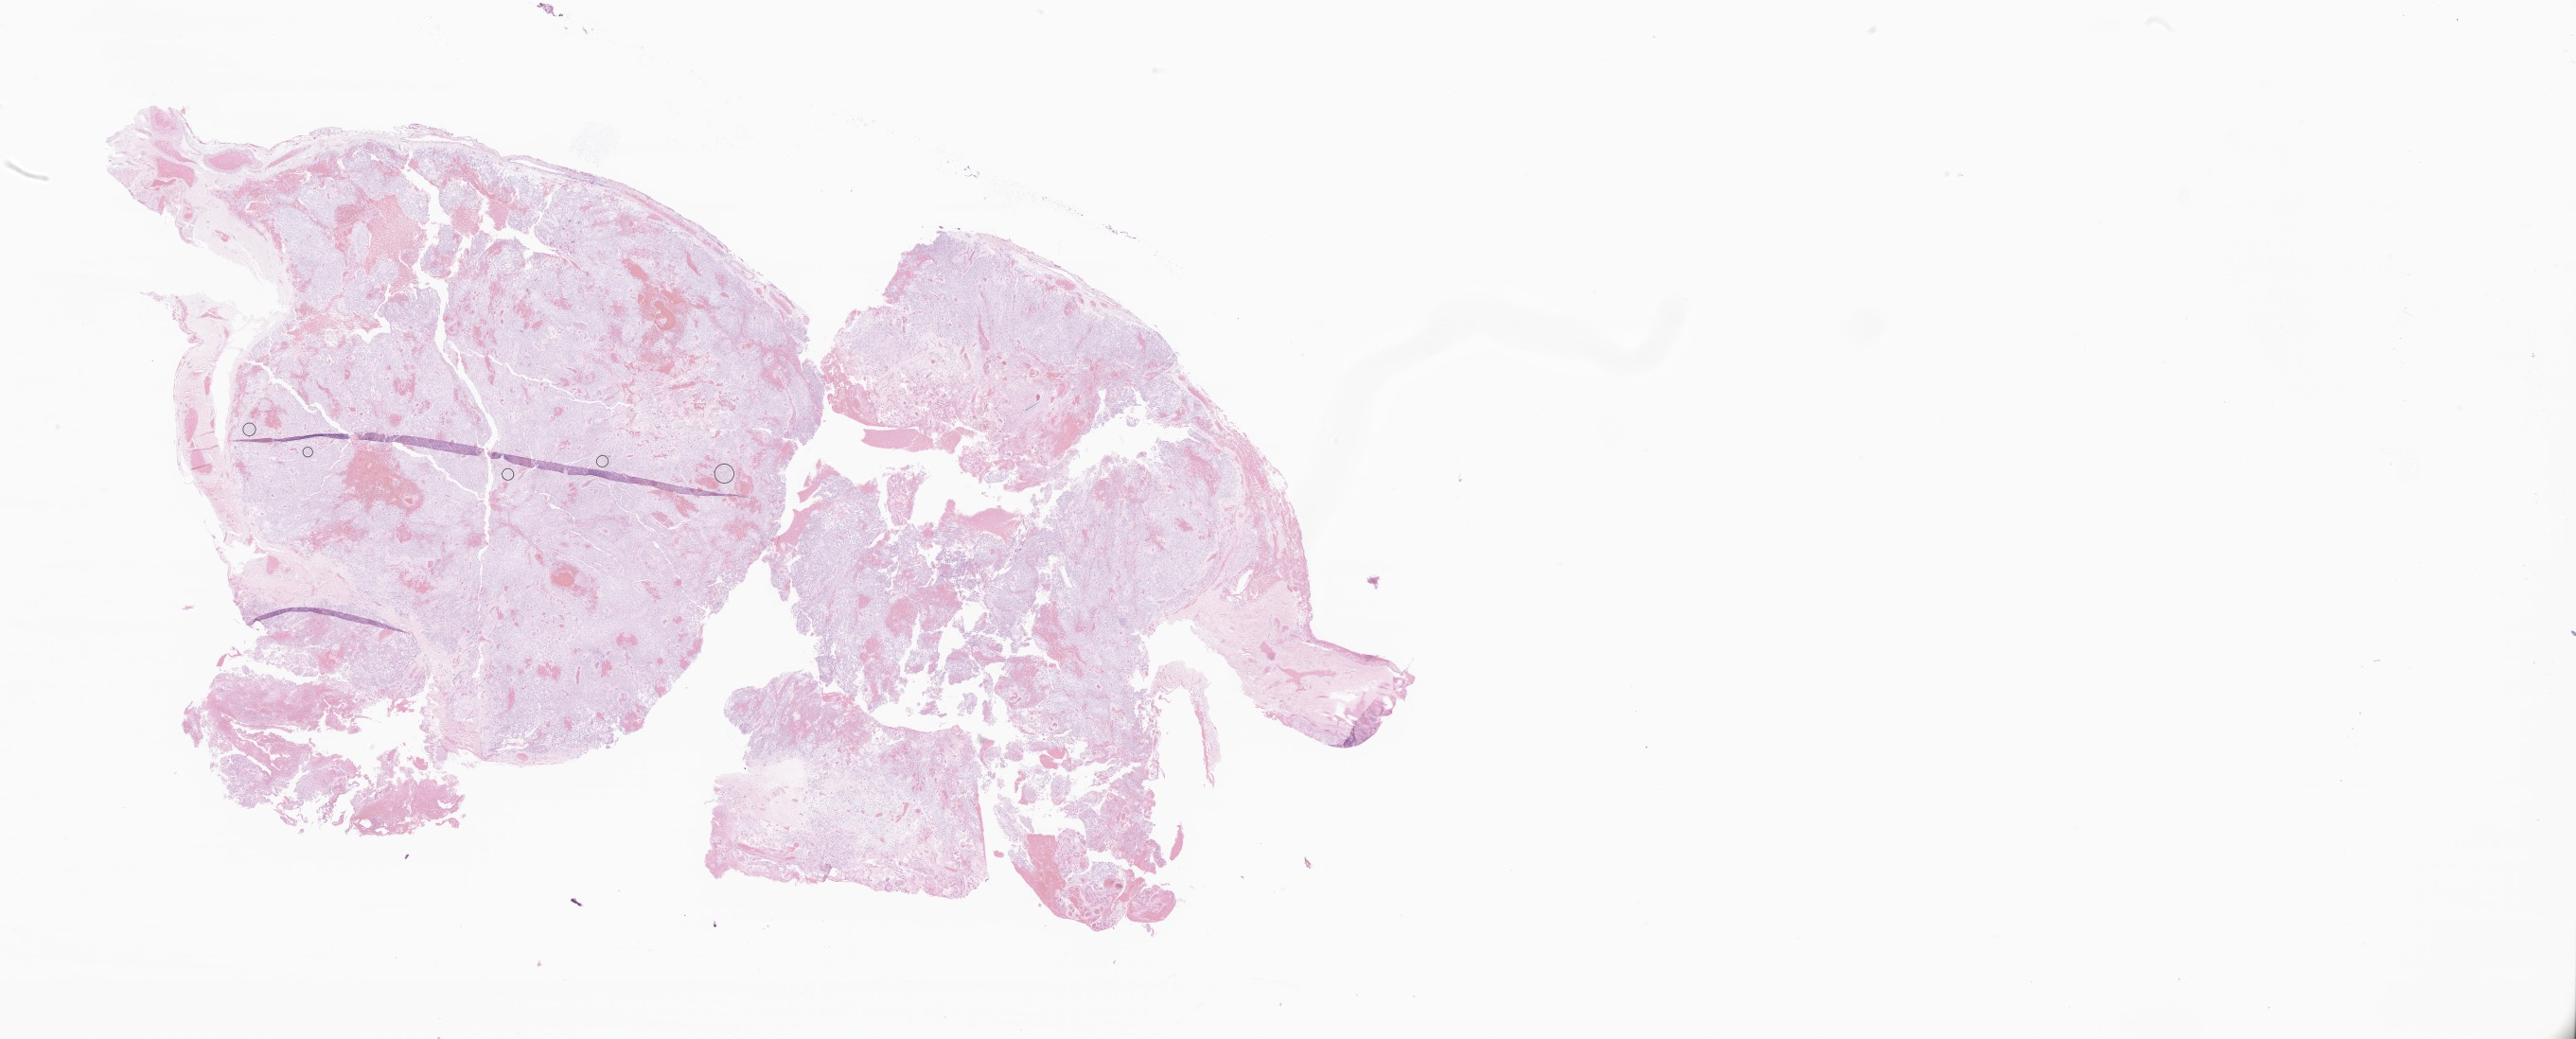
Digitized haematoxylin and eosin-stained section of tumor tissue from the spinal cord, low-resolution overview of the scanned area, about 45.9 x 18.5 mm, formalin-fixed paraffin-embedded section. Female patient, age 268 months (22 years 4 months).
Diagnosis (ICD-O-3 morphology term): Myxopapillary ependymoma.